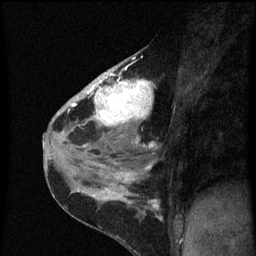
Breast MRI (dynamic contrast-enhanced), one sagittal slice. Slice 35 of 60 in the series (ordered by position). Dynamic contrast-enhanced series, image 2 of 3 at this slice position (ordered by acquisition). 1.5 T. TE 4.2 ms, TR 8 ms. 256 × 256 image matrix, field of view 180 × 180 mm. Patient: female, 38 years.
Annotated regions visible in this slice (semi-automatically segmented with operator editing):
- analysis volume of interest (the breast-tissue region the enhancement analysis was run in; not a lesion): bounding box [x1, y1, x2, y2] px = [80, 52, 155, 151]
- tumour enhancement mask (voxels above the 70 % enhancement threshold inside the analysis volume of interest): [82, 62, 155, 149]